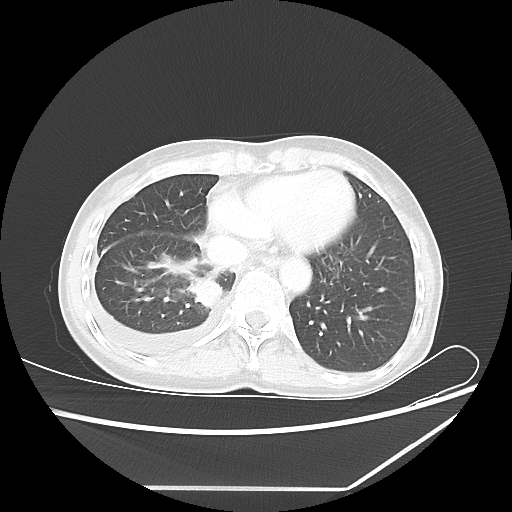
Chest CT, one axial slice. Slice 18 of 60 in the series (ordered by position). 80 kVp. Lung window (W 1500 / L -600 HU). 5 mm slice thickness. 512 × 512 image matrix, field of view 364 × 364 mm. Female patient, age 59 years. Case-level facts recorded for this patient, not image findings: clinical TNM (as recorded): T1c N1 M1.
Annotated regions visible in this slice (rectangle marked by the reading radiologist):
- lung tumour (recorded histology: adenocarcinoma): box from (x=186, y=272) to (x=227, y=311) px